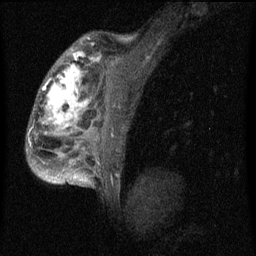
Breast MRI (dynamic contrast-enhanced), one sagittal slice; position 46 of 60 along the scan axis; dynamic contrast-enhanced series, image 2 of 4 at this slice position (ordered by acquisition); 1.5 T; TE 4.2 ms, TR 8 ms; 2 mm slice thickness; 256 × 256 image matrix. Female patient, age 50 years.
Outlined on this slice (semi-automatically segmented with operator editing):
- analysis volume of interest (the breast-tissue region the enhancement analysis was run in; not a lesion): bounding box [x1, y1, x2, y2] px = [27, 44, 124, 177]
- tumour enhancement mask (voxels above the 70 % enhancement threshold inside the analysis volume of interest): [28, 48, 101, 177]